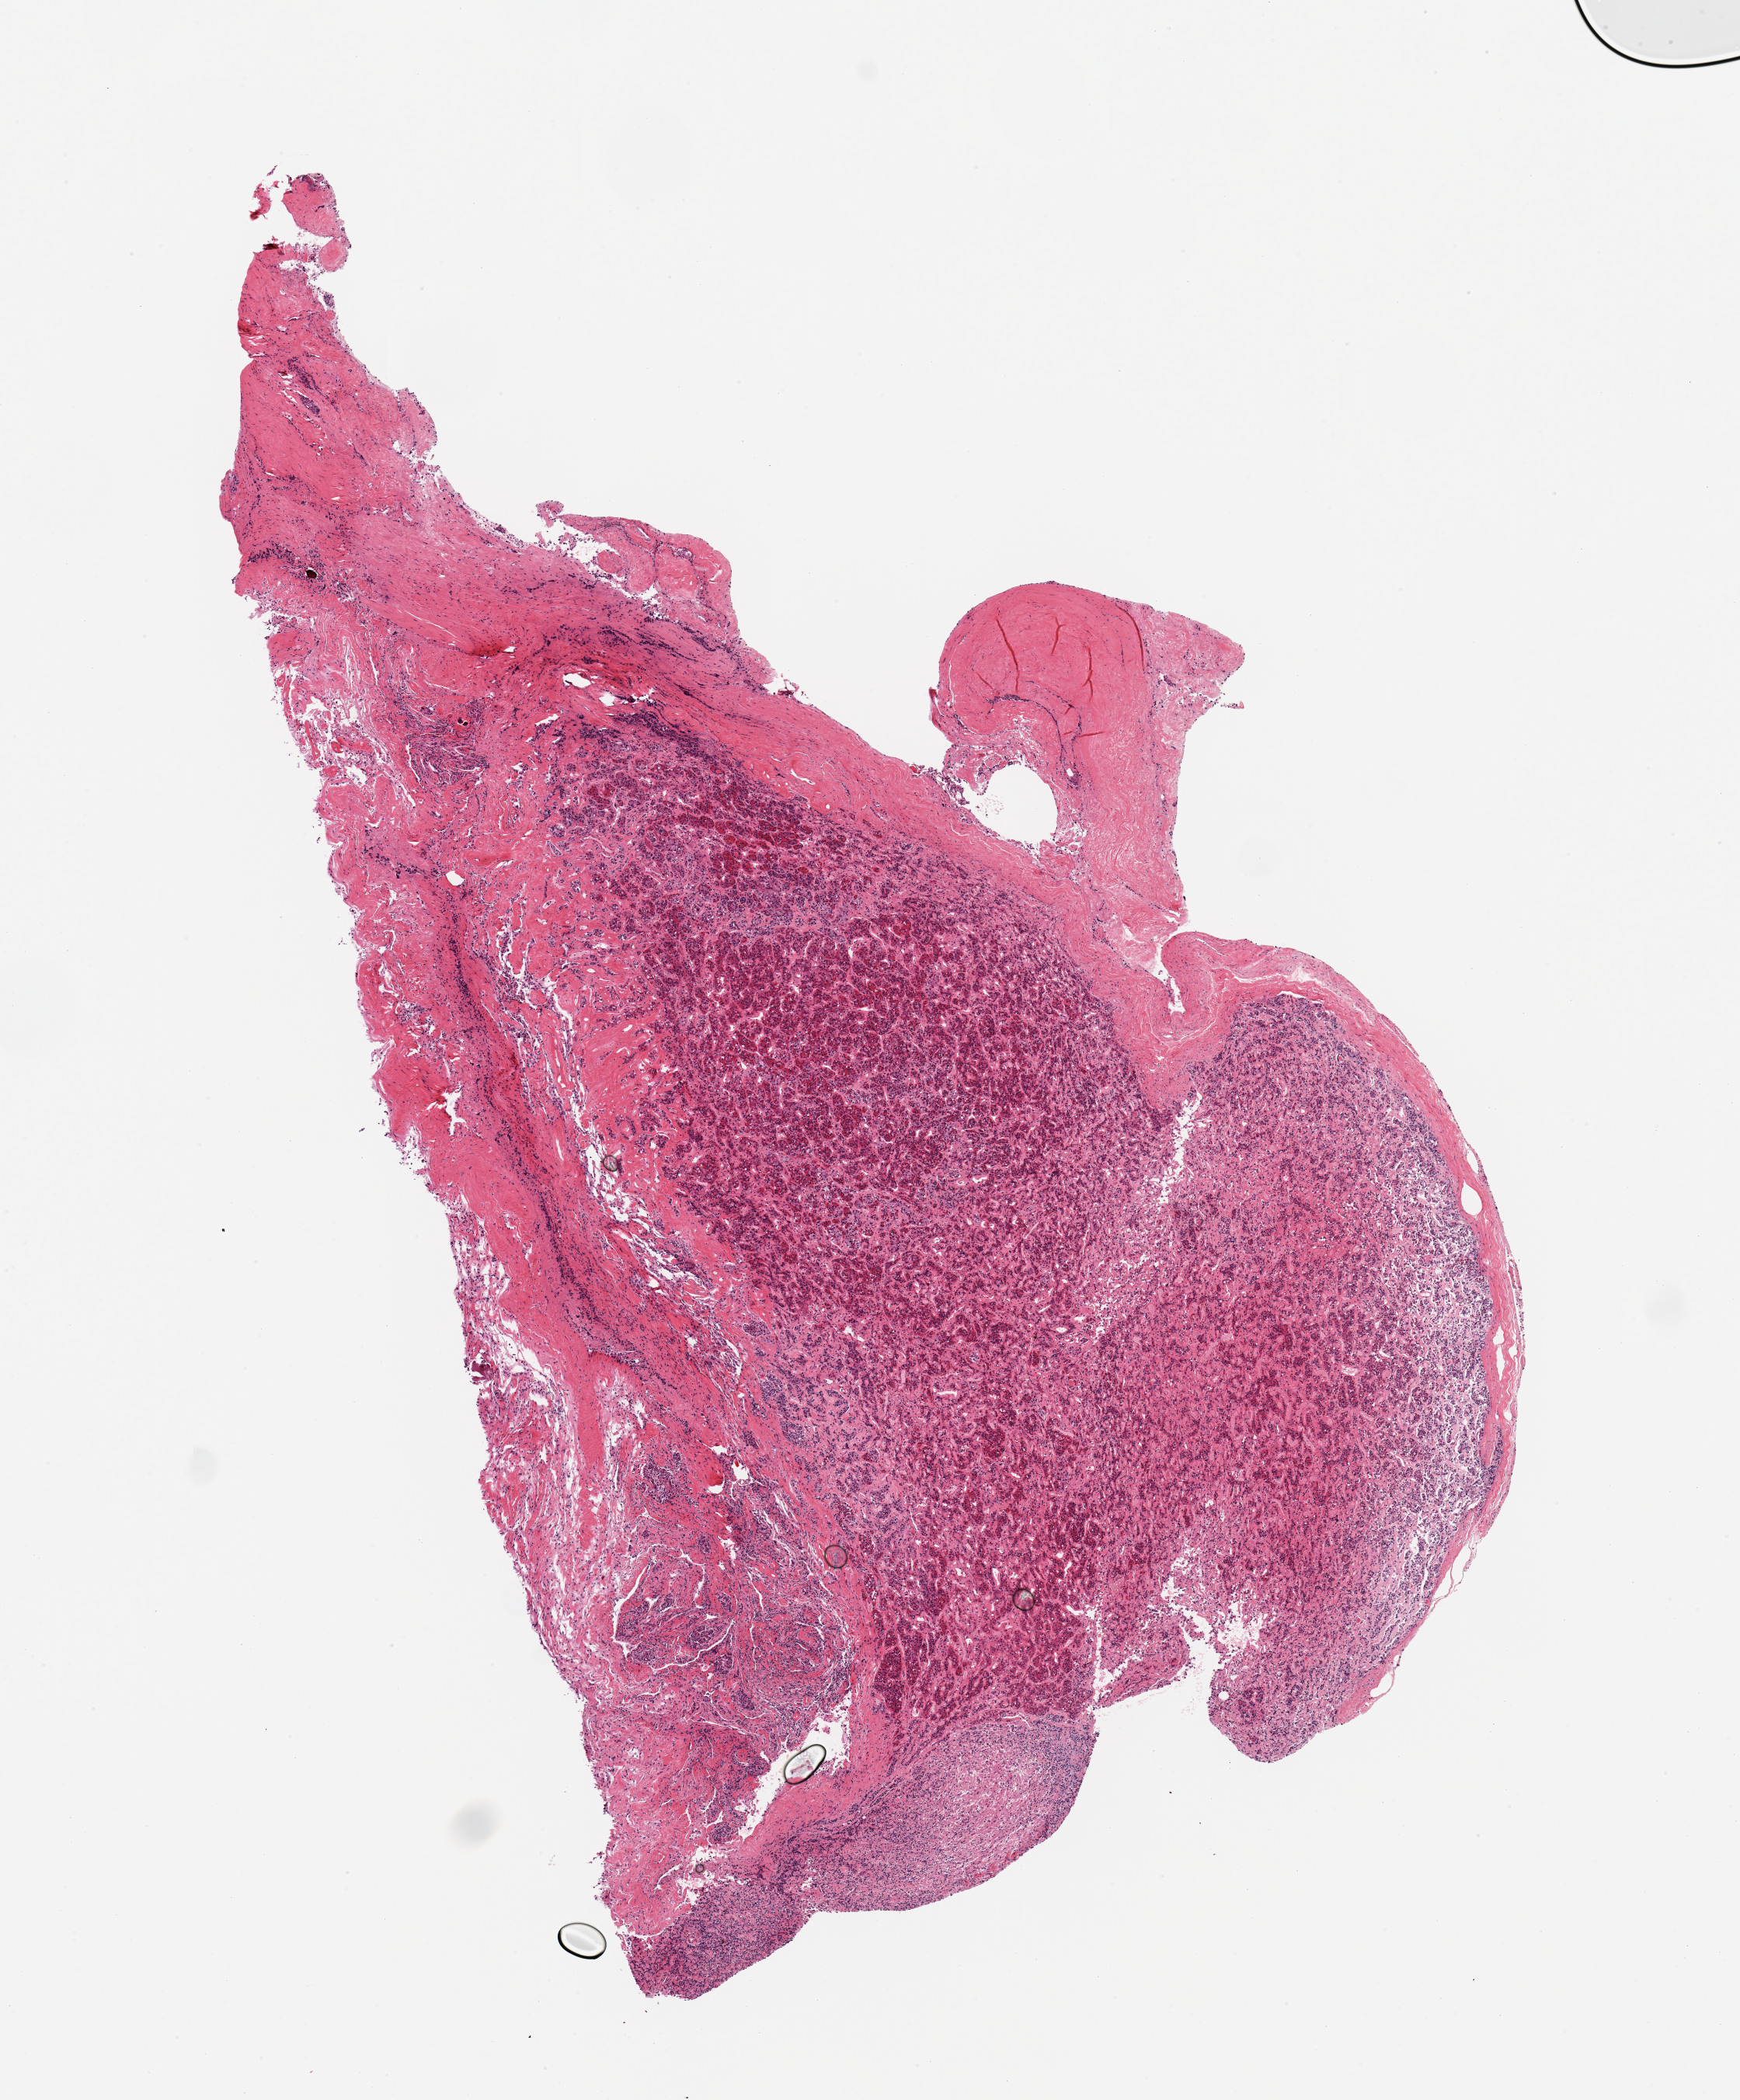
Whole-slide image, H&E stain, whole scanned area (about 8.9 x 10.7 mm) shown as a low-resolution overview; PAXgene-fixed paraffin-embedded (PFPE) section; section of pituitary (target tissue); tissue donor sample. Male donor.
Reviewer comment on this tissue sample: 1 piece, adenohypophysis and neurohypophysis.